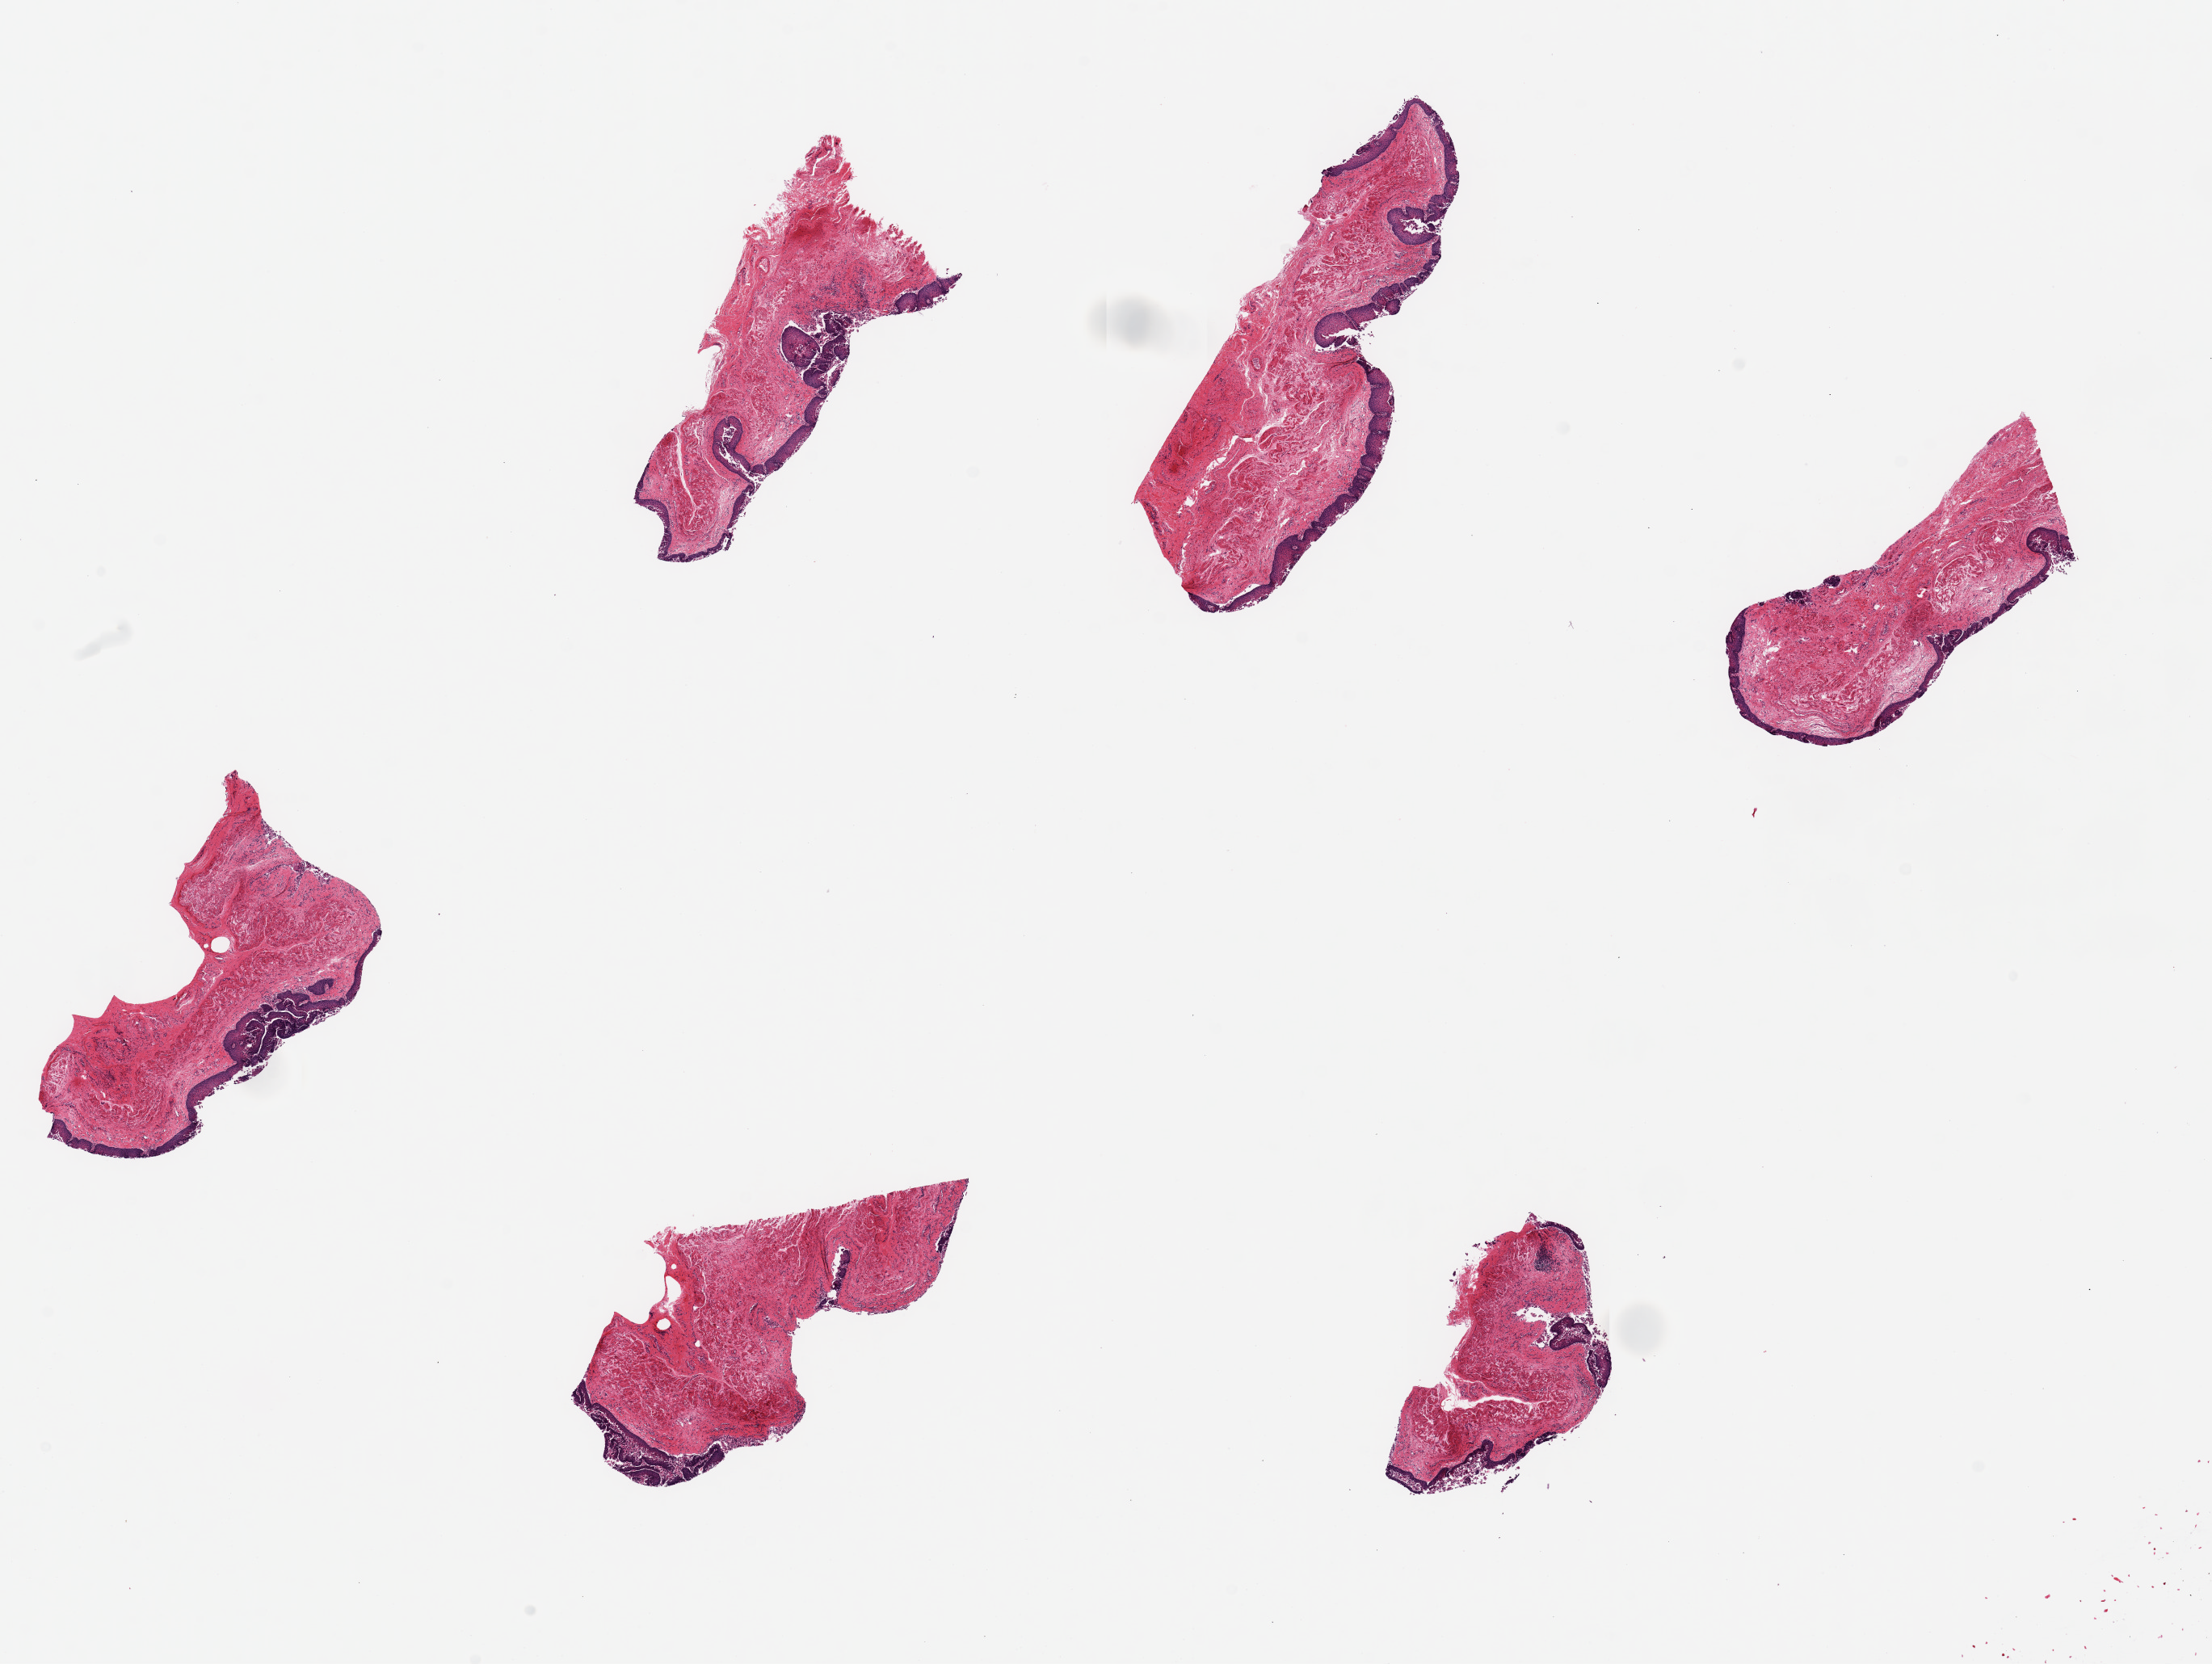
Whole-slide image, H&E stain, brightfield — whole scanned area (about 21.7 x 16.3 mm) shown as a low-resolution overview; PAXgene-fixed, paraffin-embedded tissue; section of esophageal mucous membrane (target tissue); donor tissue sample. Male donor.
* review note (as recorded): 6 pieces, up to 5x2mm; superficial sloughing of squamous mucosa